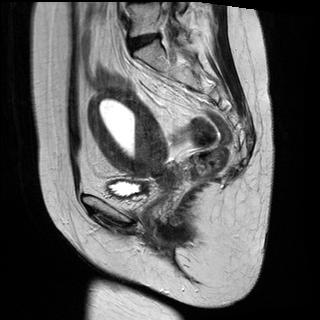
Pelvic MRI for cervical cancer, one sagittal slice; slice 11 of 28 in the series (ordered by position); T2-weighted; 1.5 T; TE 89 ms, TR 2740 ms; 4 mm slice thickness; 320 × 320 image matrix, field of view 260 × 260 mm. Female patient, age 49 years.
Annotated regions visible in this slice (manually delineated by an expert):
- uterus and cervix: bounding box [x1, y1, x2, y2] px = [88, 85, 182, 189]